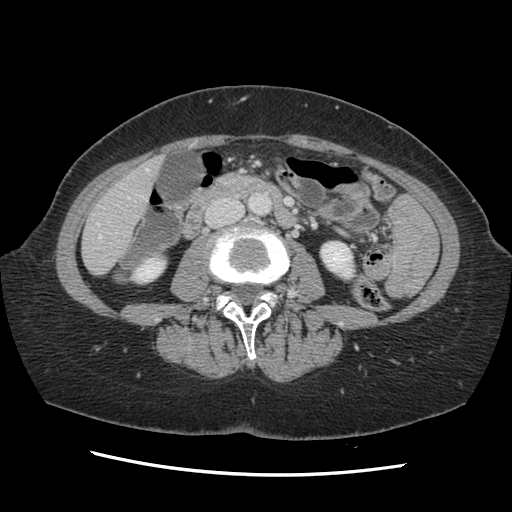
Contrast-enhanced abdominal CT, one axial slice. Slice 36 of 141 in the series (ordered by position). 120 kVp. Soft-tissue window (W 400 / L 40 HU). 2.5 mm slice thickness. 512 × 512 image matrix, field of view 330 × 330 mm. Female patient, age 61 years. From the clinical record (not read from this slice): diagnosis: colorectal cancer liver metastases, imaged before liver resection; multiple liver metastases: no; largest metastasis: 2.4 cm; disease in both lobes: no.
Outlined on this slice (outlined manually by an expert reader):
- hepatic veins: bounding box [x1, y1, x2, y2] px = [97, 169, 149, 238]
- liver: [84, 159, 161, 275]
- planned liver remnant (the part of the liver to remain after resection): [84, 163, 160, 275]